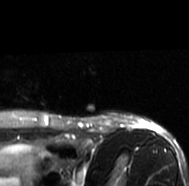
MRI of an extremity soft-tissue mass, one axial slice. Slice 62 of 77 in the series (ordered by position). T2-weighted fat-saturated. MR volume resampled by the dataset authors to the PET/CT grid (not the native acquisition matrix). 3.27 mm slice thickness. 189 × 186 image matrix, field of view 185 × 182 mm. Female patient. From the clinical record (not read from this slice): histological type: leiomyosarcoma; grade: high; site of the primary tumour: groin.
Structures marked on this image (expert contour drawn on MRI and transferred to this co-registered scan by the dataset authors):
- gross tumour volume including surrounding oedema: bounding box [x1, y1, x2, y2] px = [88, 113, 155, 133]